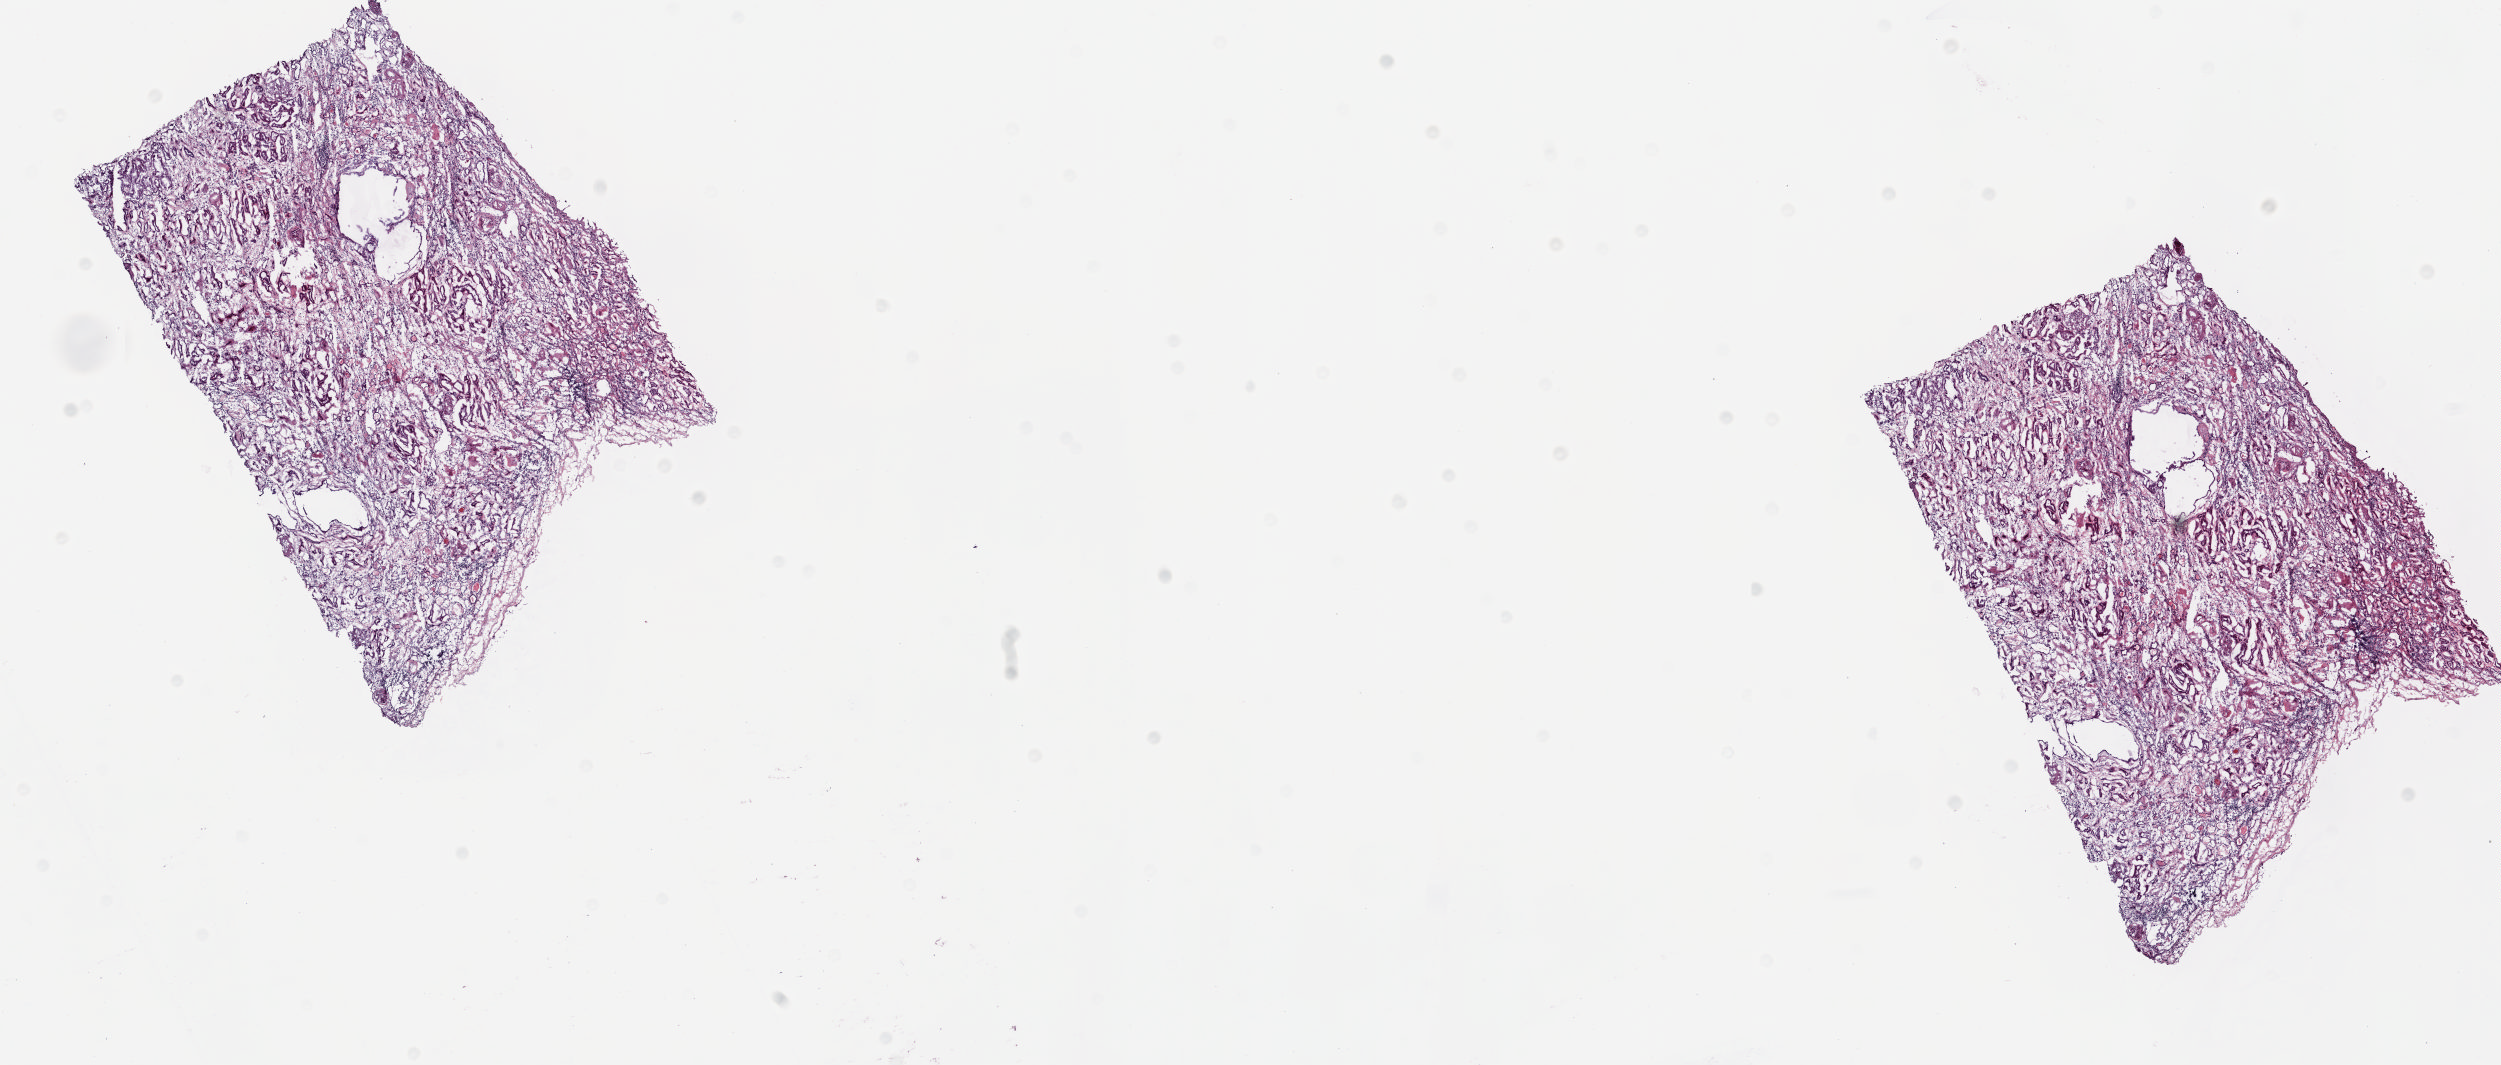
Digitized H&E-stained tissue section (whole slide), shown as a low-resolution overview of the whole scanned area (about 19.8 x 8.4 mm), frozen section, solid tissue normal (non-tumour tissue) sample from the kidney. Male, age 79 years at initial diagnosis. Composition of this section per pathologist review: tumour cells 0%, tumour nuclei 0%, normal cells 100%, stromal cells 0%, necrosis 0%. Inflammatory infiltration, as recorded: lymphocyte infiltration 10%, monocyte infiltration 4%, neutrophil infiltration 0%.
This section: solid tissue normal (non-tumour) sample from the same patient. Patient diagnosis: Papillary adenocarcinoma, NOS.